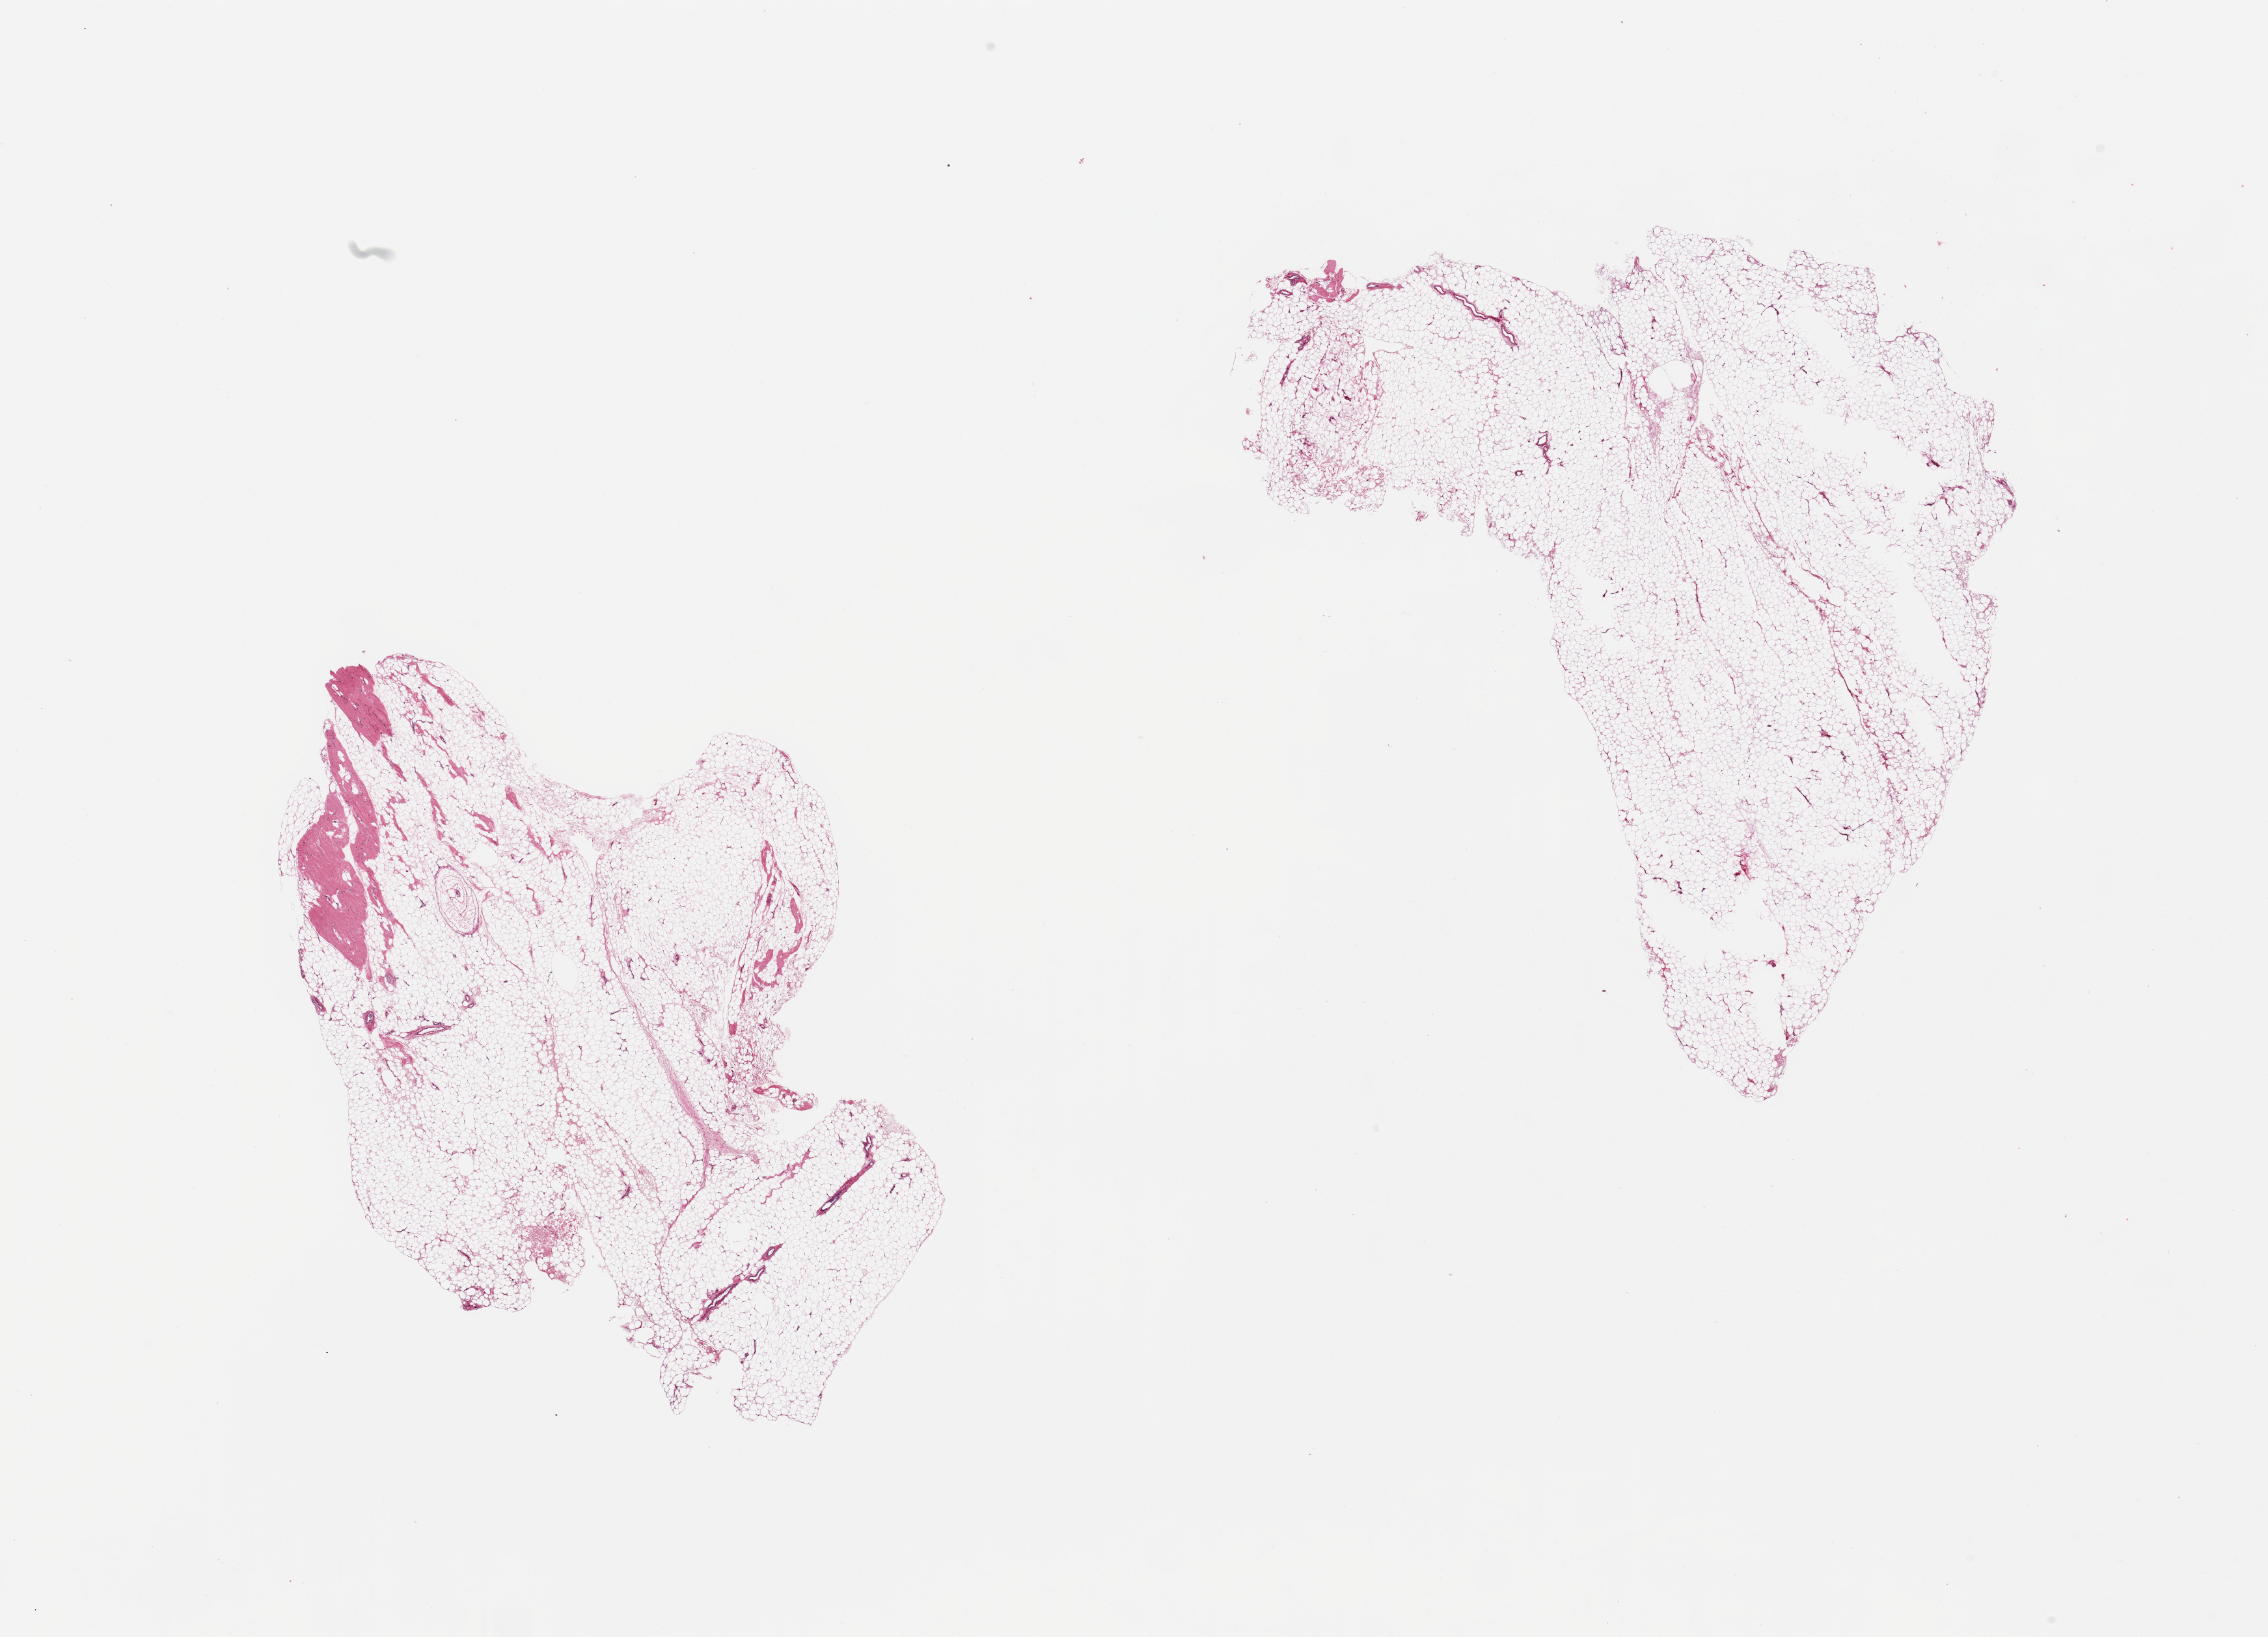
Whole-slide image, haematoxylin and eosin stain, brightfield — shown as a low-resolution overview of the whole scanned area (about 27.6 x 19.9 mm), PAXgene-fixed, paraffin-embedded tissue, target tissue: adipose tissue, donor tissue sample. Donor: male.
• reviewer comment on this tissue sample: 2 pieces; 1 has 10% stromal content